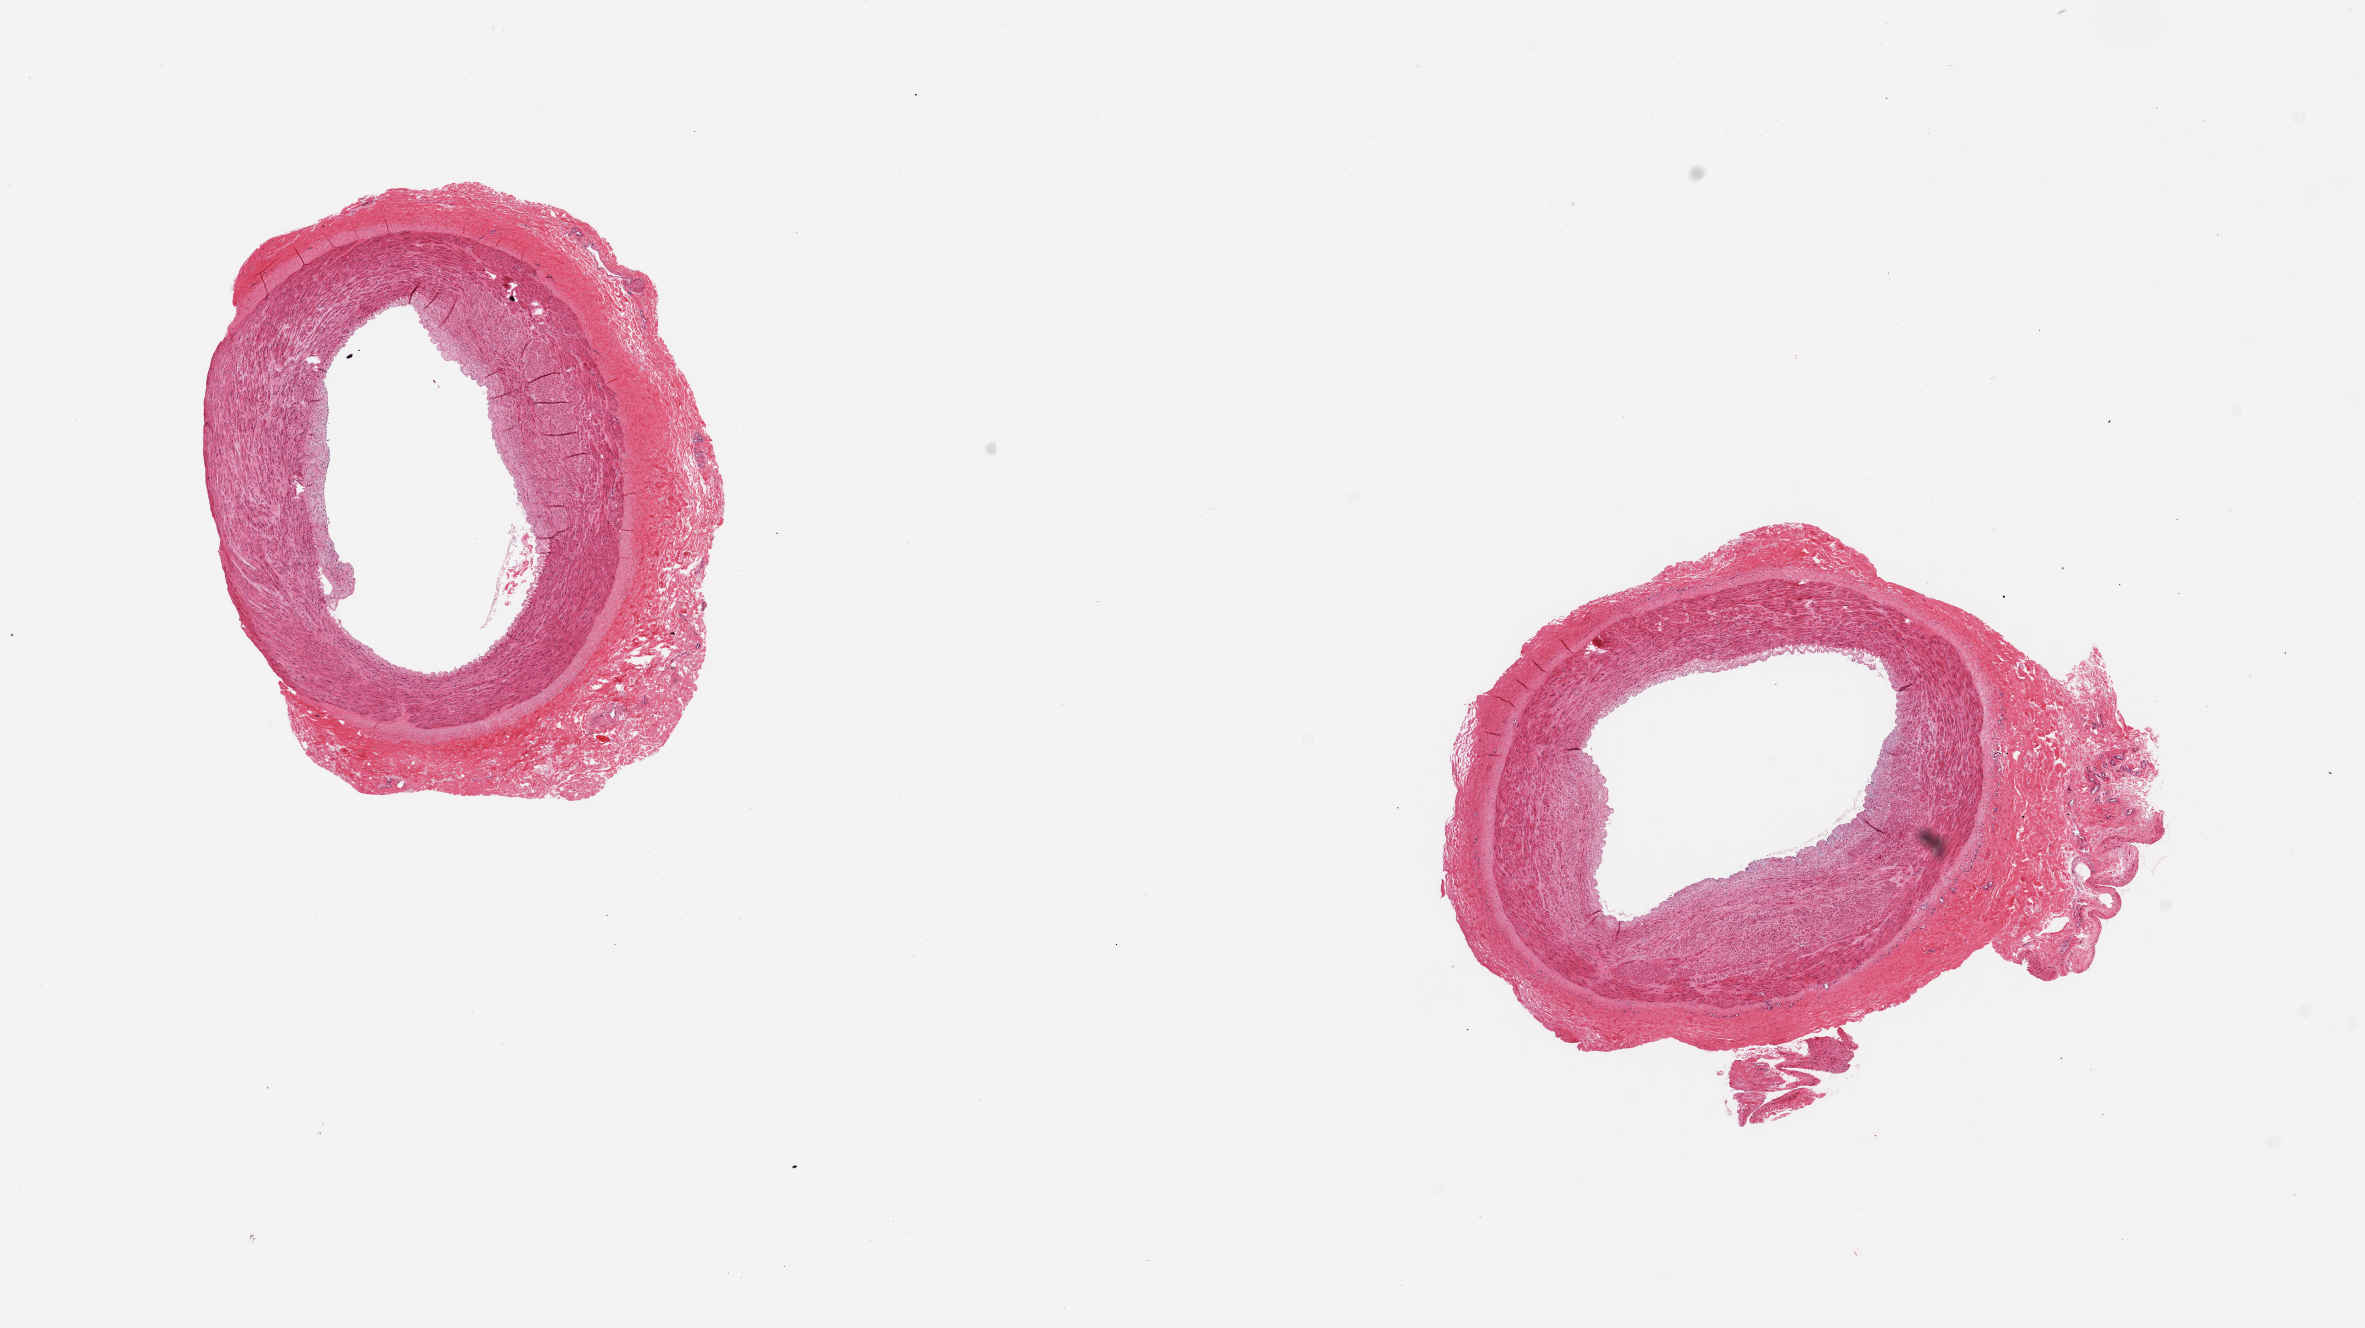
Whole-slide image, H&E stain, brightfield, a low-resolution overview of the entire scanned area, about 18.7 x 10.5 mm. PAXgene-fixed, paraffin-embedded tissue. Section of tibial artery (target tissue). Donor tissue sample. Male donor.
Review note (as recorded): 2 pieces ~4mm. Adherent rim of fibrous tissue circmferentially on both, ~0.5mm--1mm.